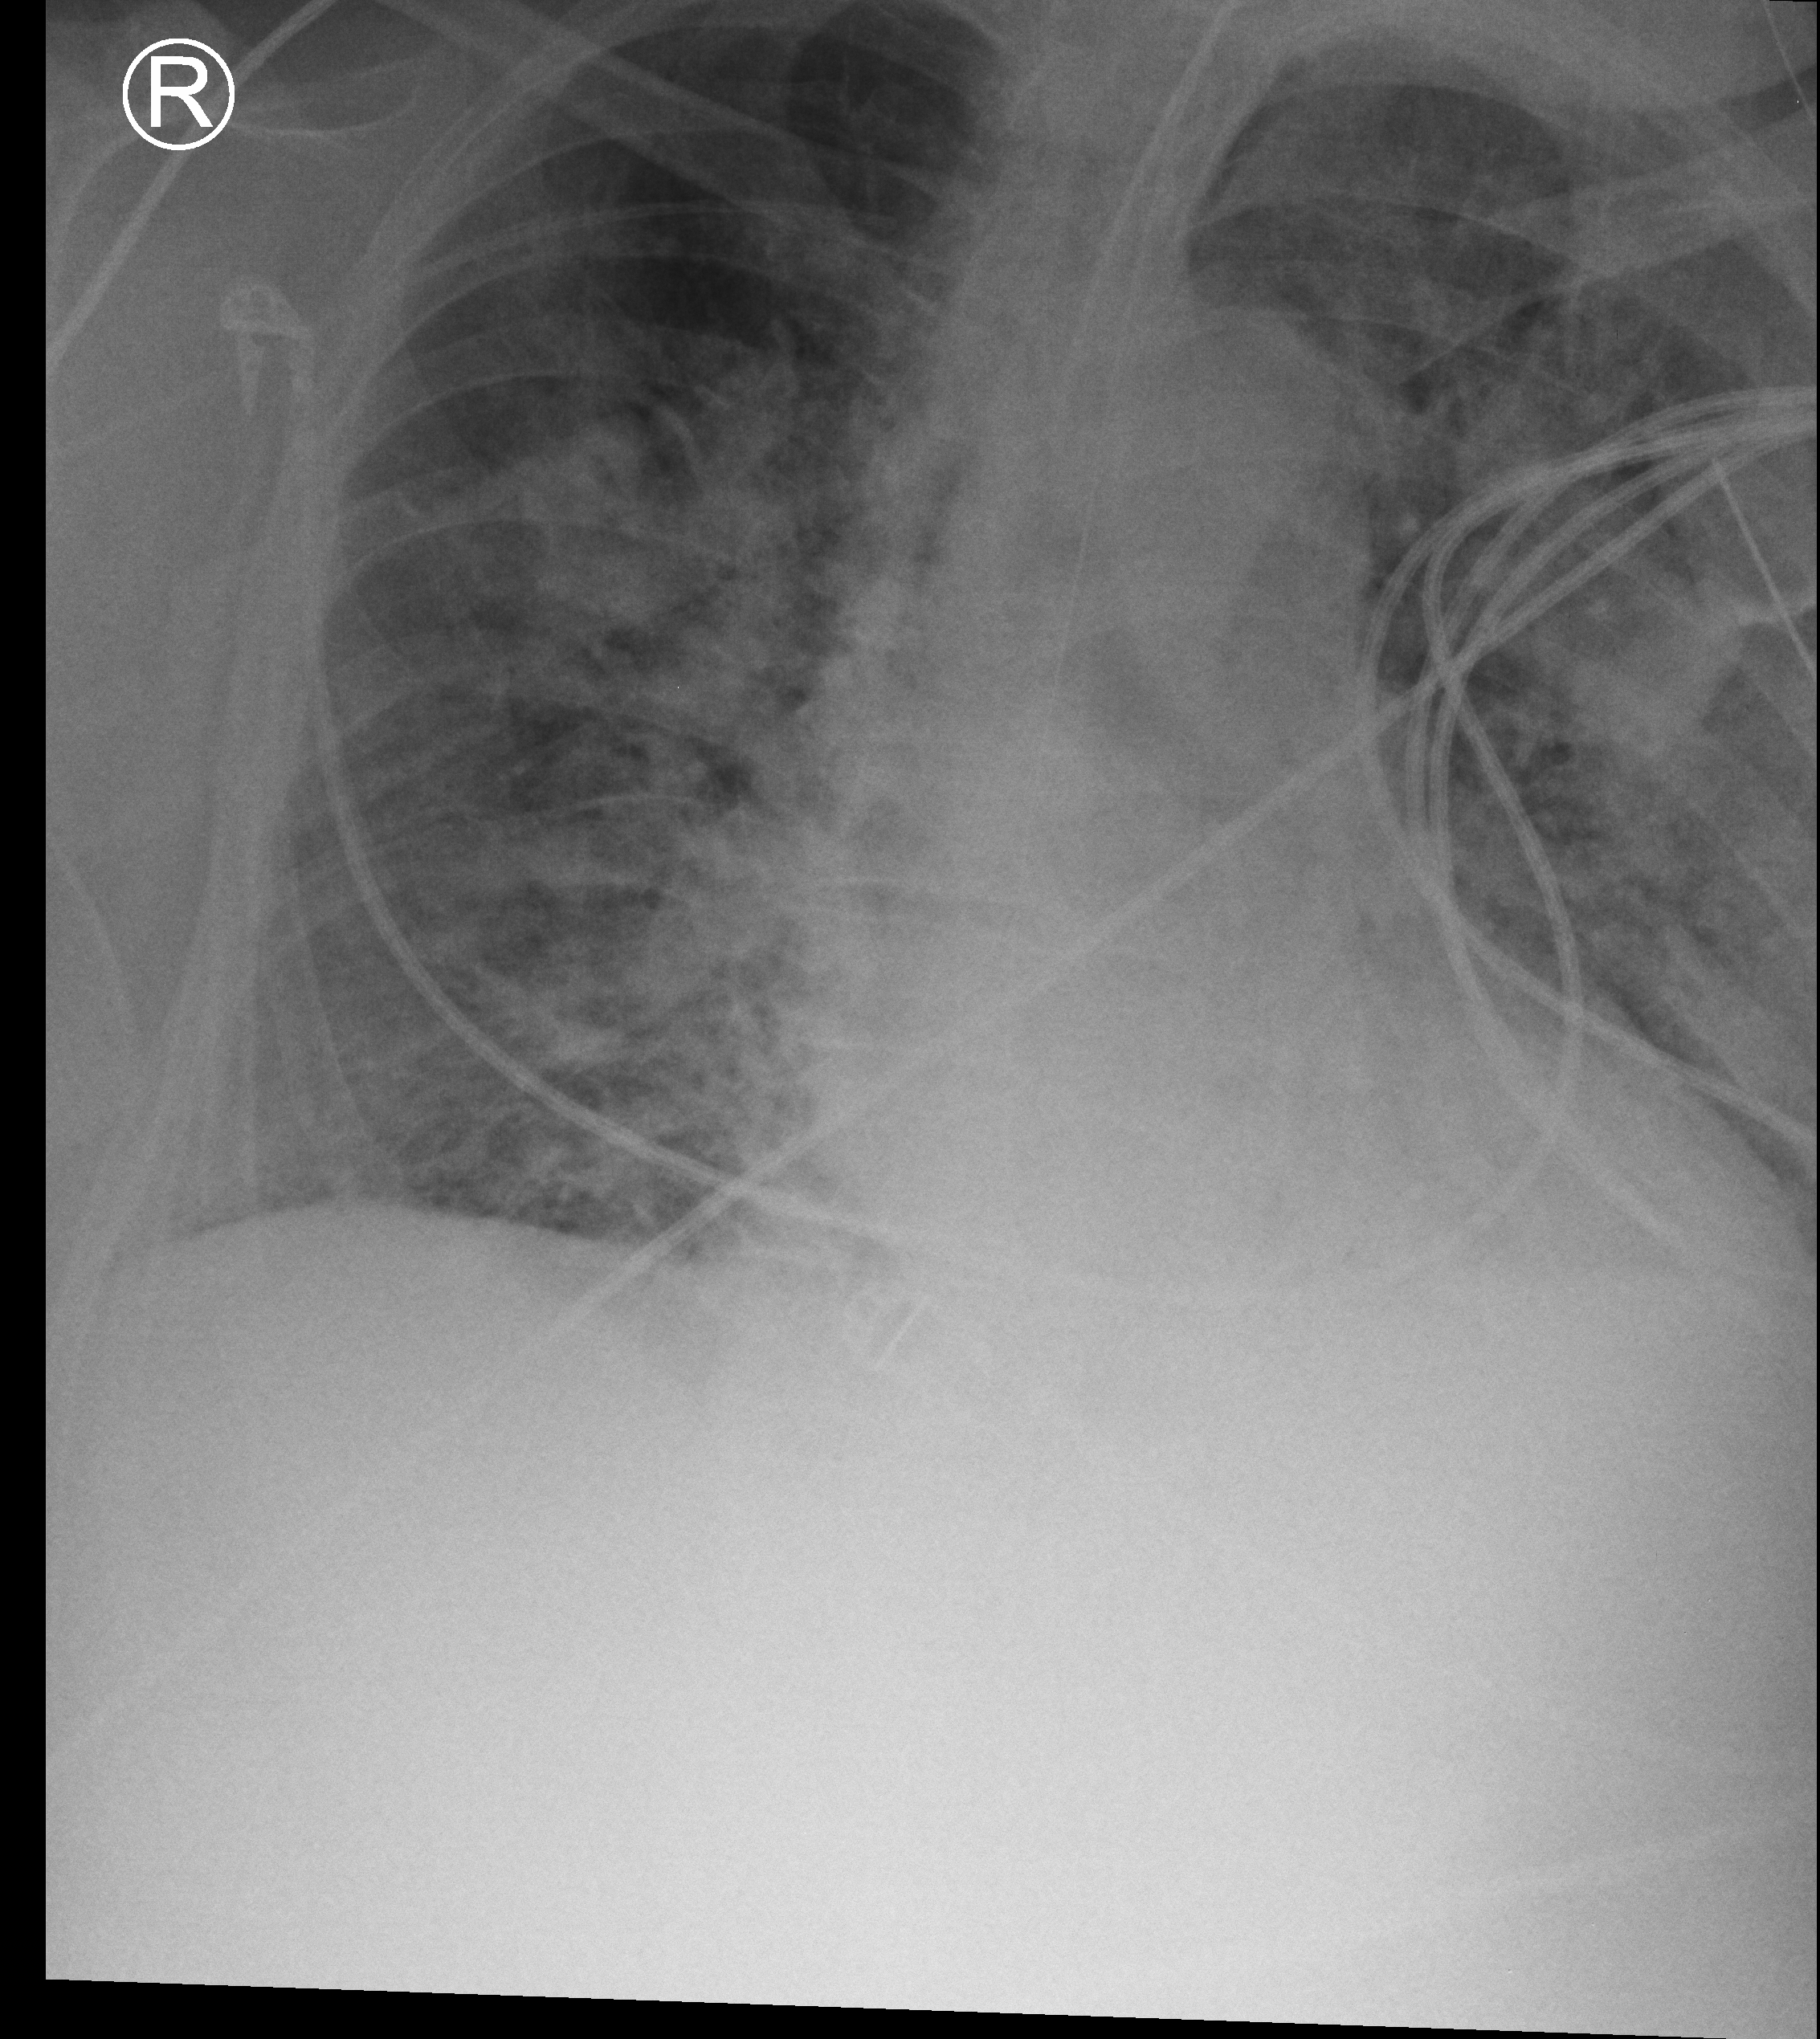
Bedside chest radiograph (computed radiography); anteroposterior (AP) projection. Male patient hospitalised with COVID-19, age 60–74 years.
Admission-level facts for this patient (not findings on this image; timing relative to this image not recorded): mechanically ventilated during this hospital stay: yes.